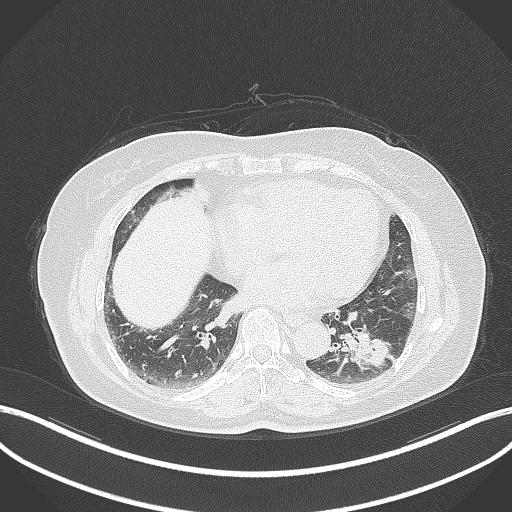
Chest CT, one axial slice; position 141 of 311 along the scan axis; 120 kVp; lung window (W 1500 / L -600 HU); 1 mm slice thickness; 512 × 512 image matrix, field of view 400 × 400 mm. Patient: female, 59 years. Case-level facts recorded for this patient, not image findings: clinical TNM (as recorded): T2a N0 M0.
Outlined on this slice (rectangle marked by the reading radiologist):
- lung tumour (recorded histology: adenocarcinoma): bounding box <339,323,393,370> (left, top, right, bottom; pixels)